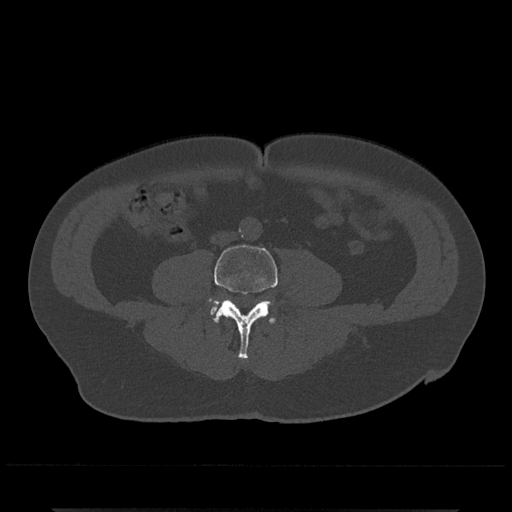
CT including the spine, one axial slice. Slice 145 of 797 in the series (ordered by position). 120 kVp. Bone window (W 1800 / L 400 HU). 0.5 mm slice thickness. 512 × 512 image matrix, field of view 393 × 393 mm. Patient: male, 67 years. Case-level facts recorded for this patient, not image findings: primary cancer: prostate.
Outlined on this slice (semi-automatic segmentation, software-assisted and operator-edited):
- L4 vertebra: box from (x=208, y=244) to (x=278, y=359) px
- L5 vertebra: (x=210, y=304)–(x=274, y=315)